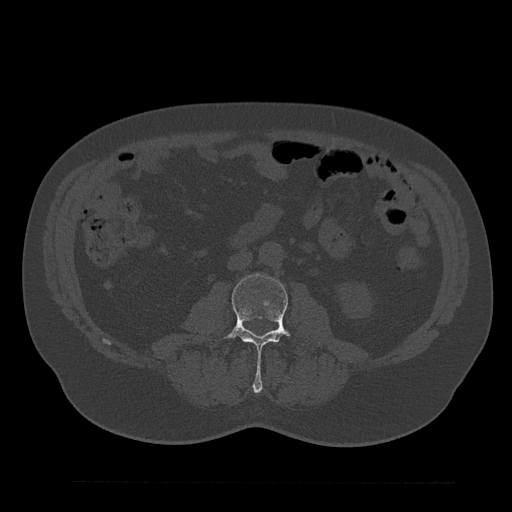
CT including the spine, one axial slice. Position 31 of 797 along the scan axis. 120 kVp. Bone window (W 1800 / L 400 HU). 0.5 mm slice thickness. 512 × 512 image matrix. Patient: male, 61 years. Case-level facts recorded for this patient, not image findings: primary cancer: prostate.
Structures marked on this image (semi-automatically segmented with operator editing):
- L3 vertebra: bounding box [x1, y1, x2, y2] px = [201, 274, 319, 393]